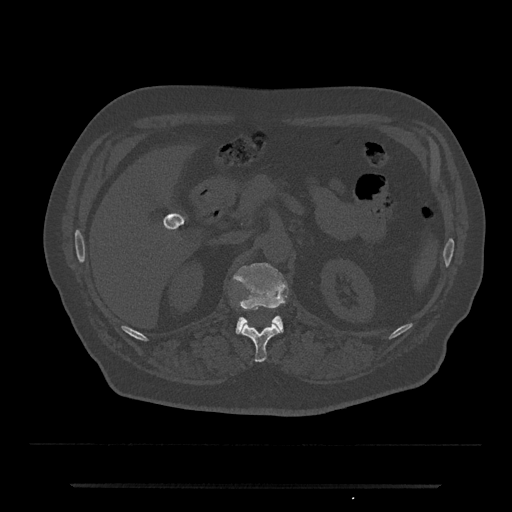
CT including the spine, one axial slice. Slice 567 of 797 in the series (ordered by position). Reconstruction kernel Br40s/3. 120 kVp. Bone window (W 1800 / L 400 HU). 0.5 mm slice thickness. 512 × 512 image matrix, field of view 434 × 434 mm. Patient: male, 80 years. Case-level facts recorded for this patient, not image findings: primary cancer: prostate.
Structures marked on this image (semi-automatic segmentation, software-assisted and operator-edited):
- L1 vertebra: bounding box (x1, y1, x2, y2) in pixels: (233, 263, 288, 334)
- T12 vertebra: (242, 324, 281, 362)